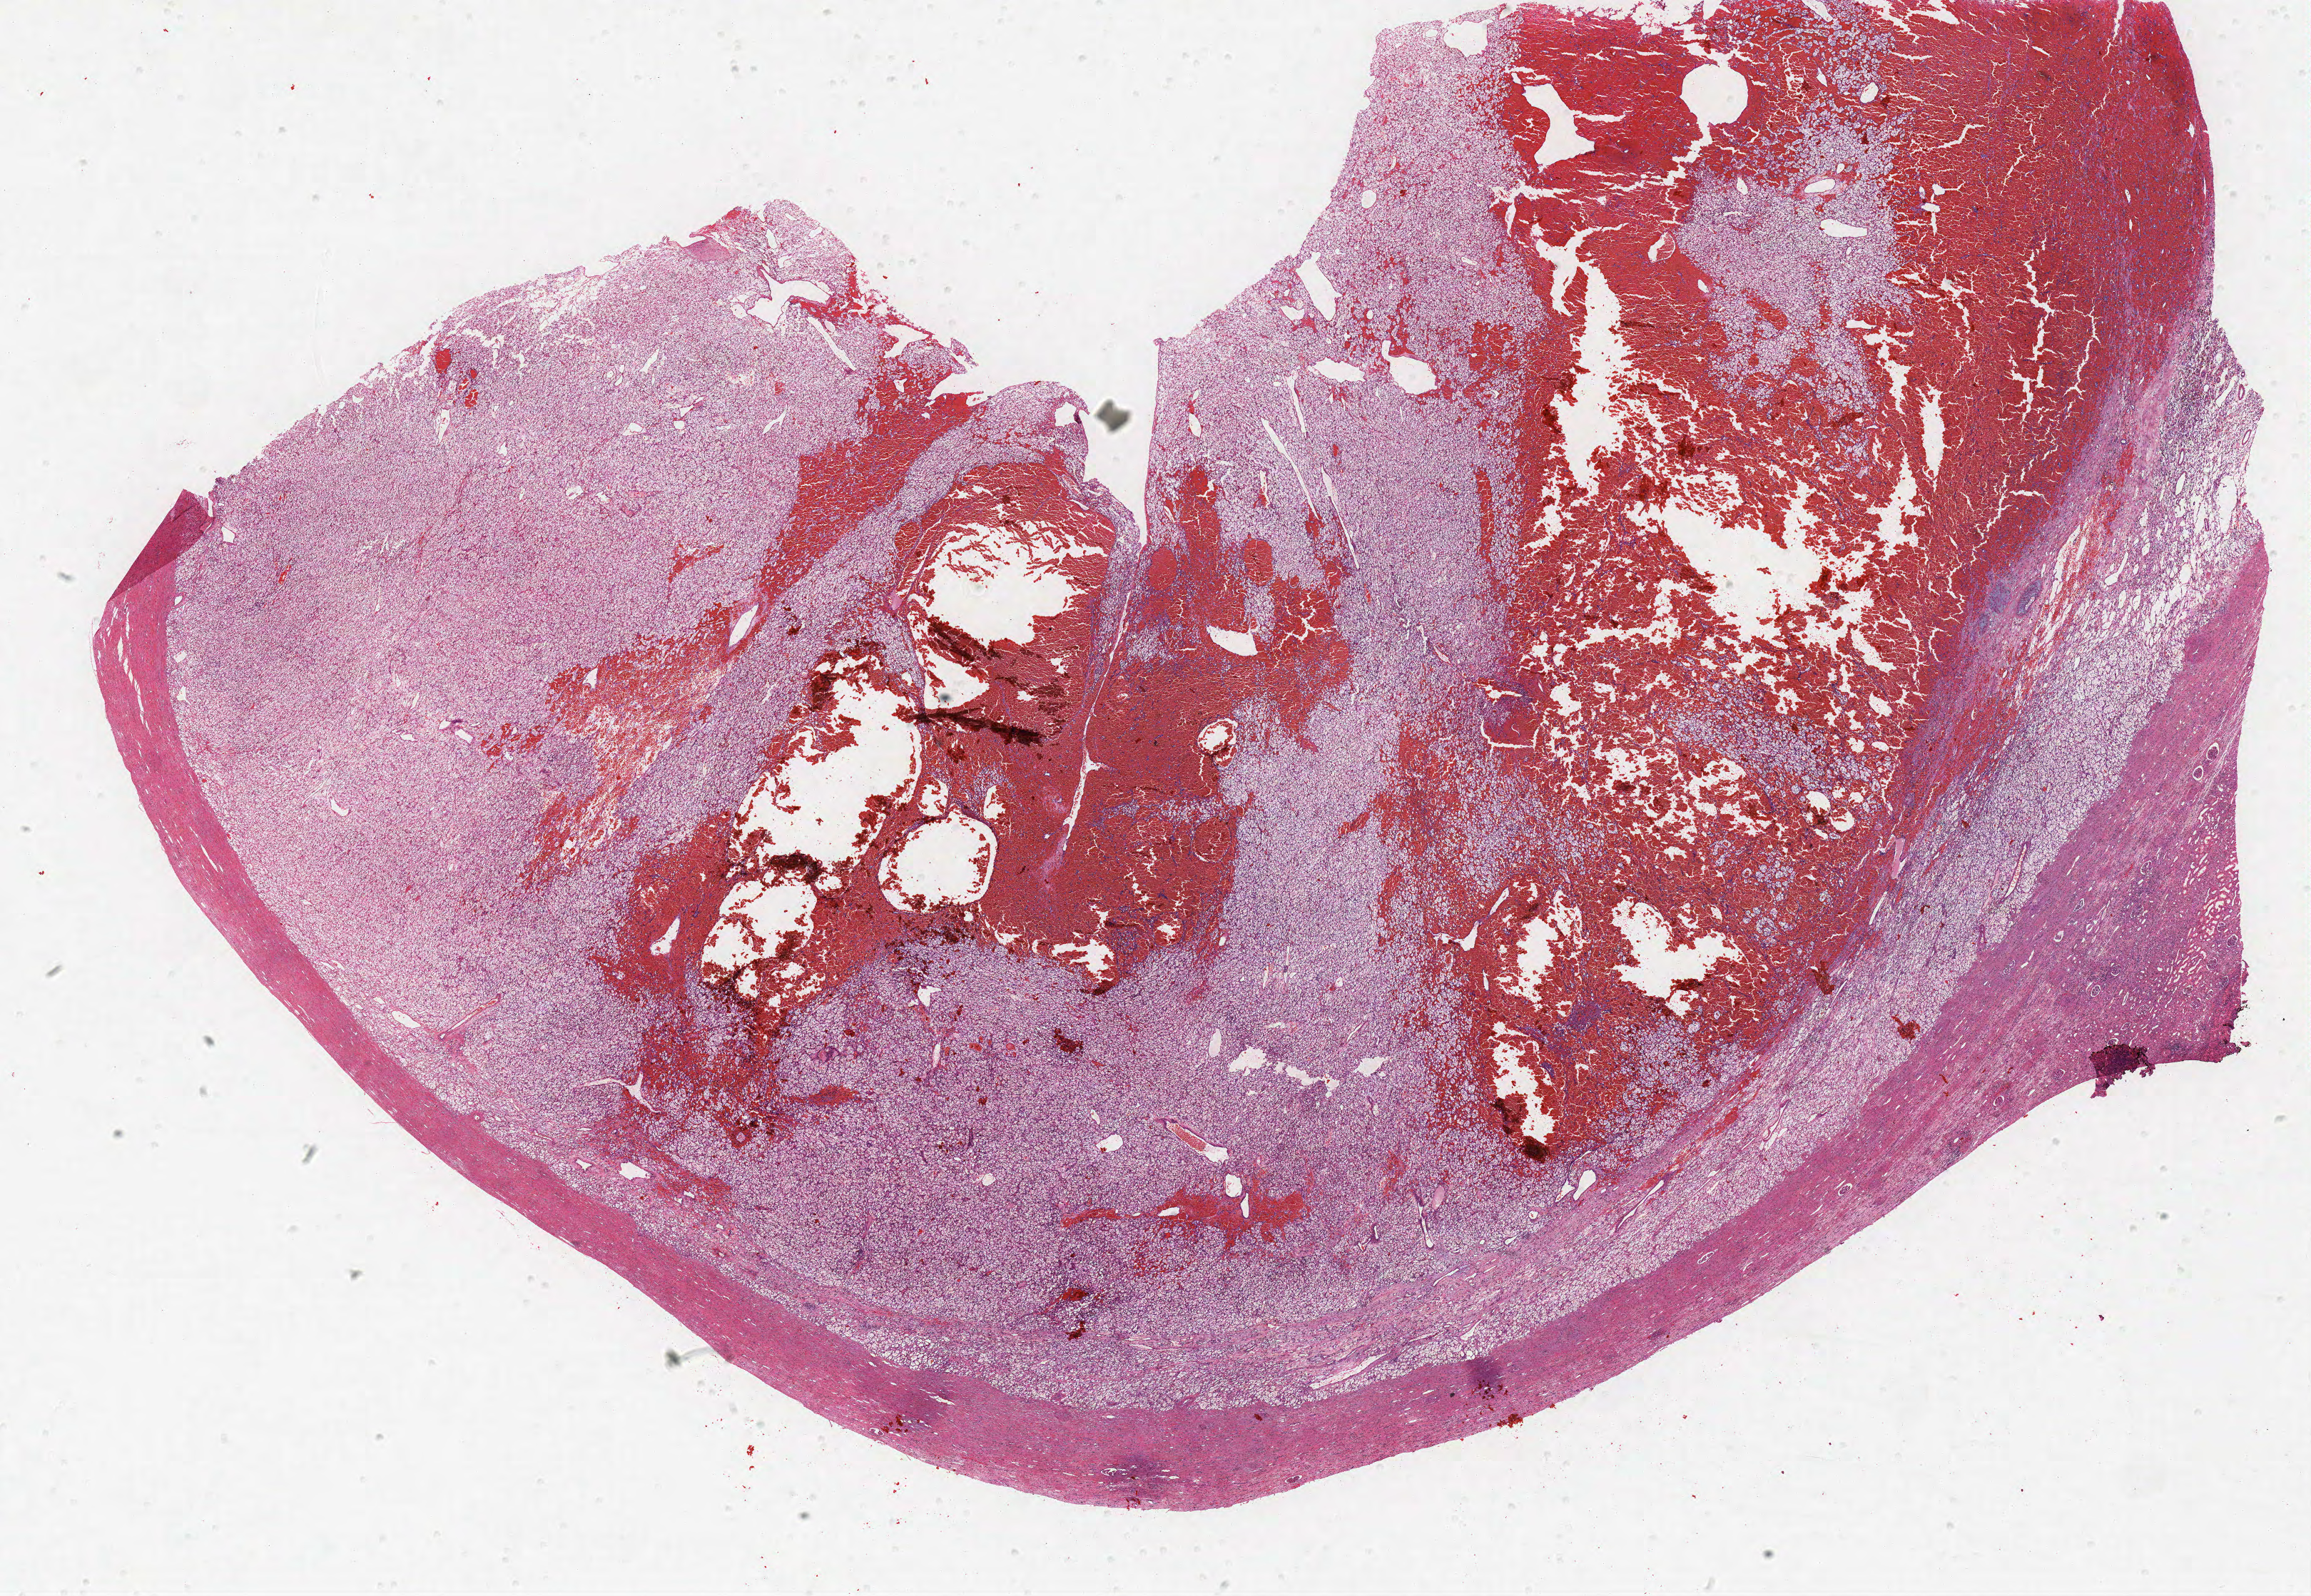
H&E-stained whole-slide image, a low-resolution overview of the entire scanned area, about 25.9 x 17.9 mm, formalin-fixed paraffin-embedded (FFPE) diagnostic section, primary tumour sample from the kidney. Female patient; age at initial diagnosis 57 years. Histologic grade: G2 (moderately differentiated).
AJCC pathologic stage: I. TNM: T1a NX M0. Pathologic diagnosis: Clear cell adenocarcinoma, NOS.